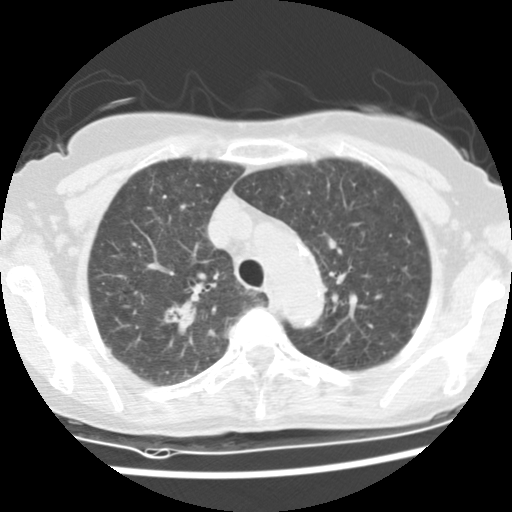
Low-dose screening chest CT, one axial slice; position 105 of 134 along the scan axis; 120 kVp; lung window (W 1500 / L -600 HU); 2.5 mm slice thickness; 512 × 512 image matrix.
Outlined on this slice (expert manual segmentation):
- lesion 1 (tumor, upper lobe of right lung): bounding box [x1, y1, x2, y2] px = [164, 299, 197, 337]